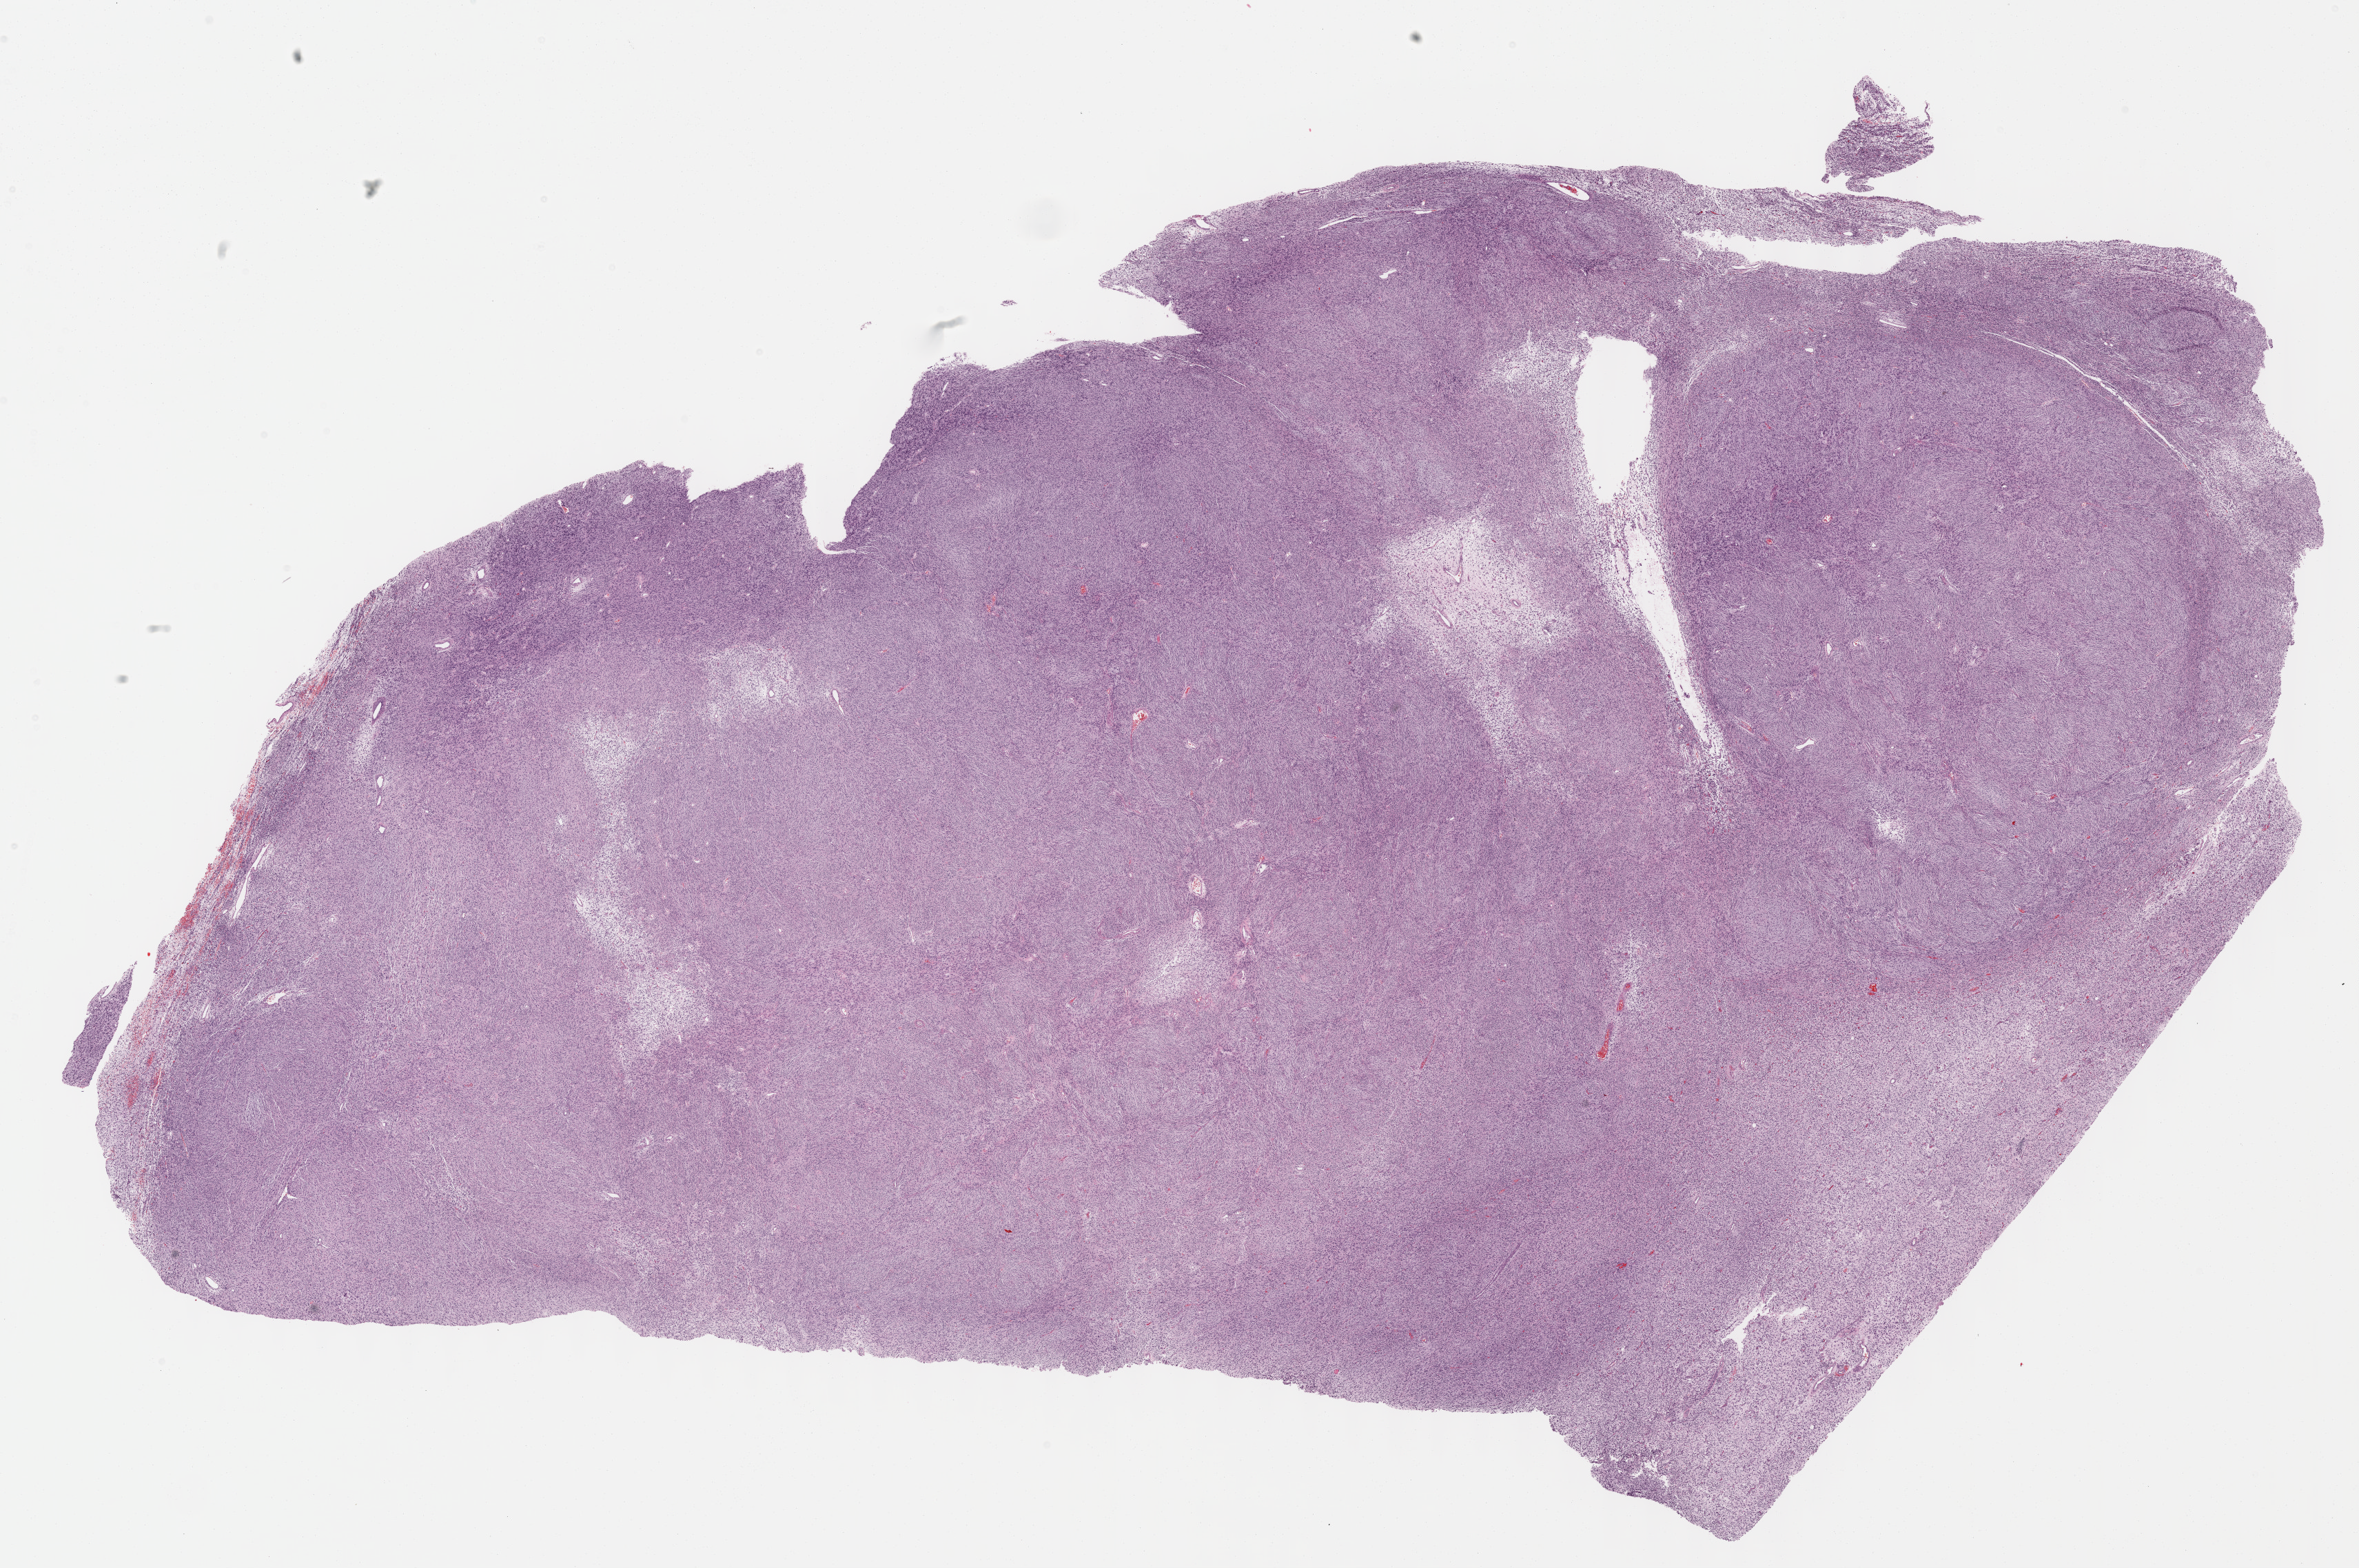
Whole-slide histology image, H&E-stained, shown as a low-resolution overview of the whole scanned area (about 27.7 x 18.4 mm, acquisition: 40x scan). Formalin-fixed paraffin-embedded (FFPE) diagnostic section. Retroperitoneum and peritoneum, primary tumour sample. Patient: male, age at initial diagnosis 66 years.
Diagnosis: Dedifferentiated liposarcoma (retroperitoneum).